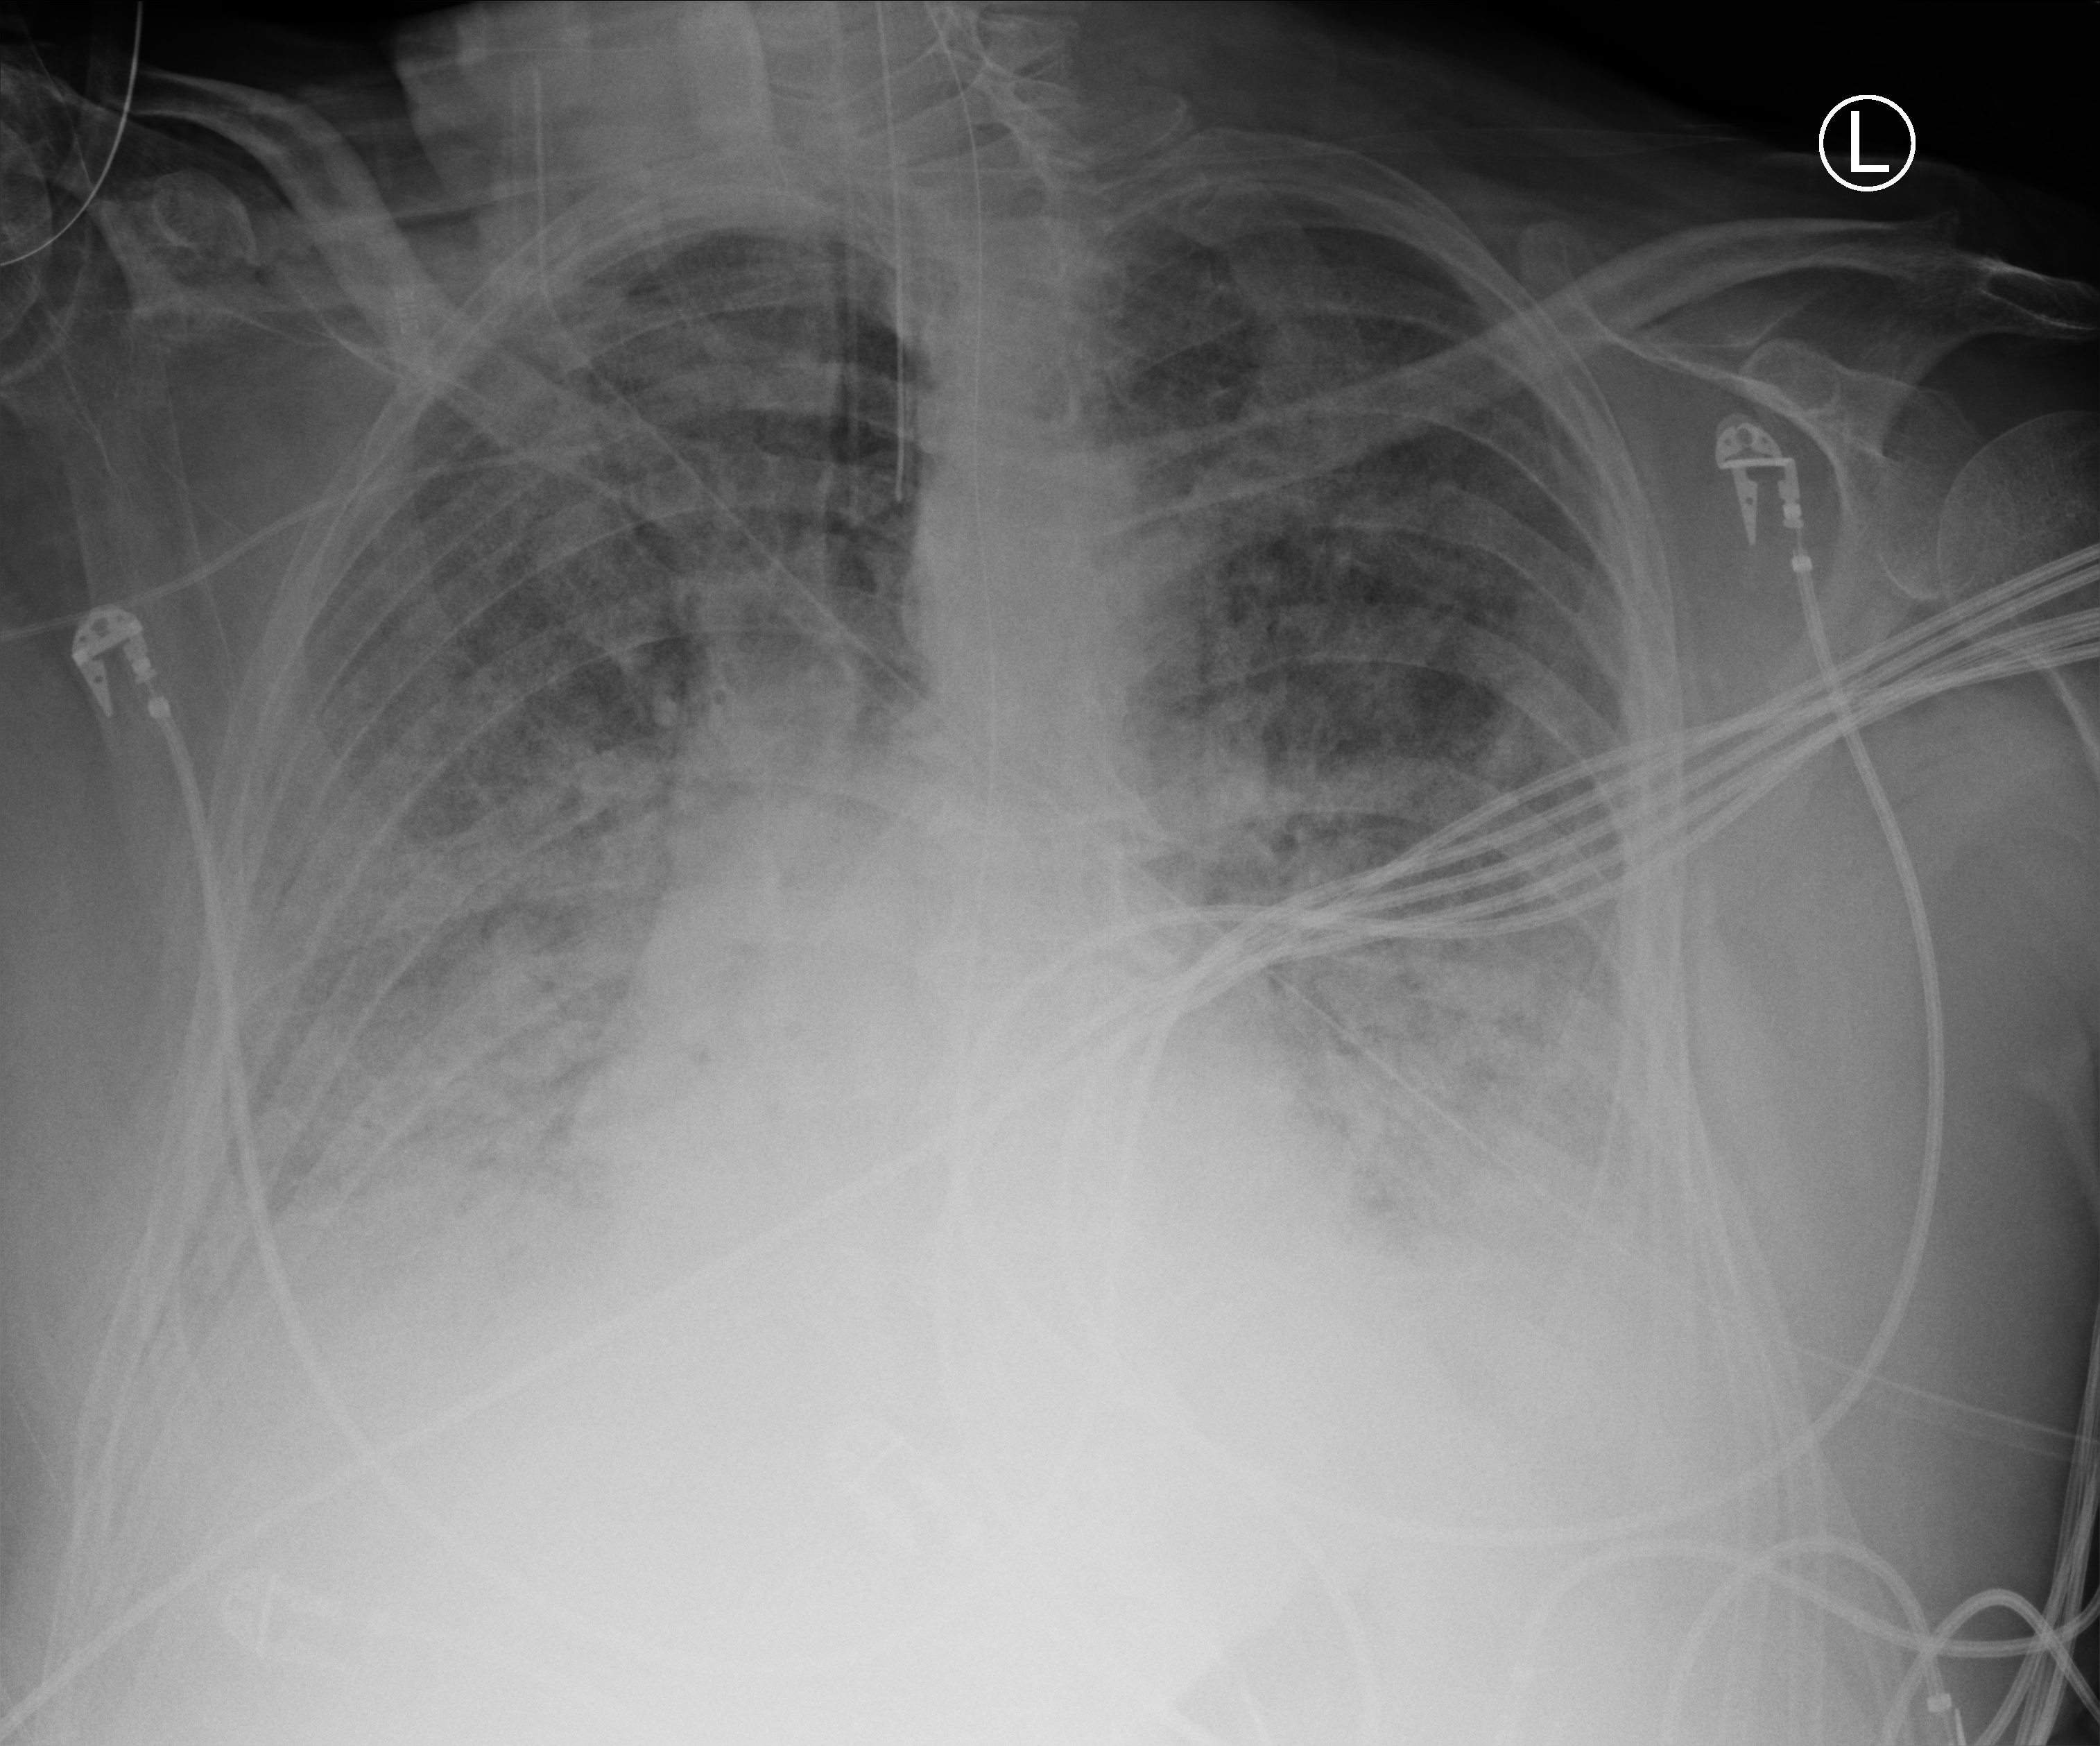
Portable chest radiograph. Patient hospitalised with COVID-19; male, aged 60–74 years.
Hospital-stay facts (about this admission, not read from this image; timing relative to this image not recorded): admitted to intensive care during this hospital stay: yes; length of hospital stay: 20 days; mechanically ventilated during this hospital stay: yes.